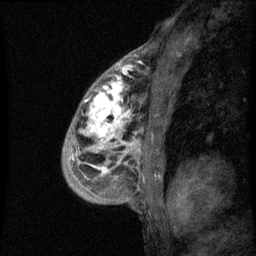
Breast MRI (dynamic contrast-enhanced), one sagittal slice; position 39 of 60 along the scan axis; dynamic contrast-enhanced series, image 2 of 3 at this slice position (ordered by acquisition); 1.5 T; TE 4.2 ms, TR 8 ms; 2 mm slice thickness; 256 × 256 image matrix, field of view 180 × 180 mm. Patient: female, 50 years.
Outlined on this slice (semi-automatic segmentation, software-assisted and operator-edited):
- analysis volume of interest (the breast-tissue region the enhancement analysis was run in; not a lesion): bounding box [x1, y1, x2, y2] px = [66, 64, 141, 187]
- tumour enhancement mask (voxels above the 70 % enhancement threshold inside the analysis volume of interest): [72, 64, 134, 175]